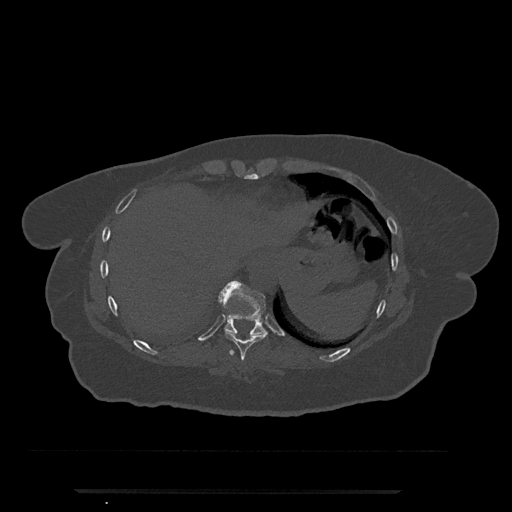
CT including the spine, one axial slice. Slice 316 of 797 in the series (ordered by position). Reconstruction kernel Br40s/3. Bone window (W 1800 / L 400 HU). 0.5 mm slice thickness. 512 × 512 image matrix, field of view 440 × 440 mm. Female patient, age 51 years. From the clinical record (not read from this slice): primary cancer: neuro; vertebrae with lytic lesions (as recorded): T8.
Structures marked on this image (semi-automatic segmentation, software-assisted and operator-edited):
- T10 vertebra: box from (x=218, y=281) to (x=267, y=336) px
- T9 vertebra: (x=225, y=331)–(x=268, y=361)